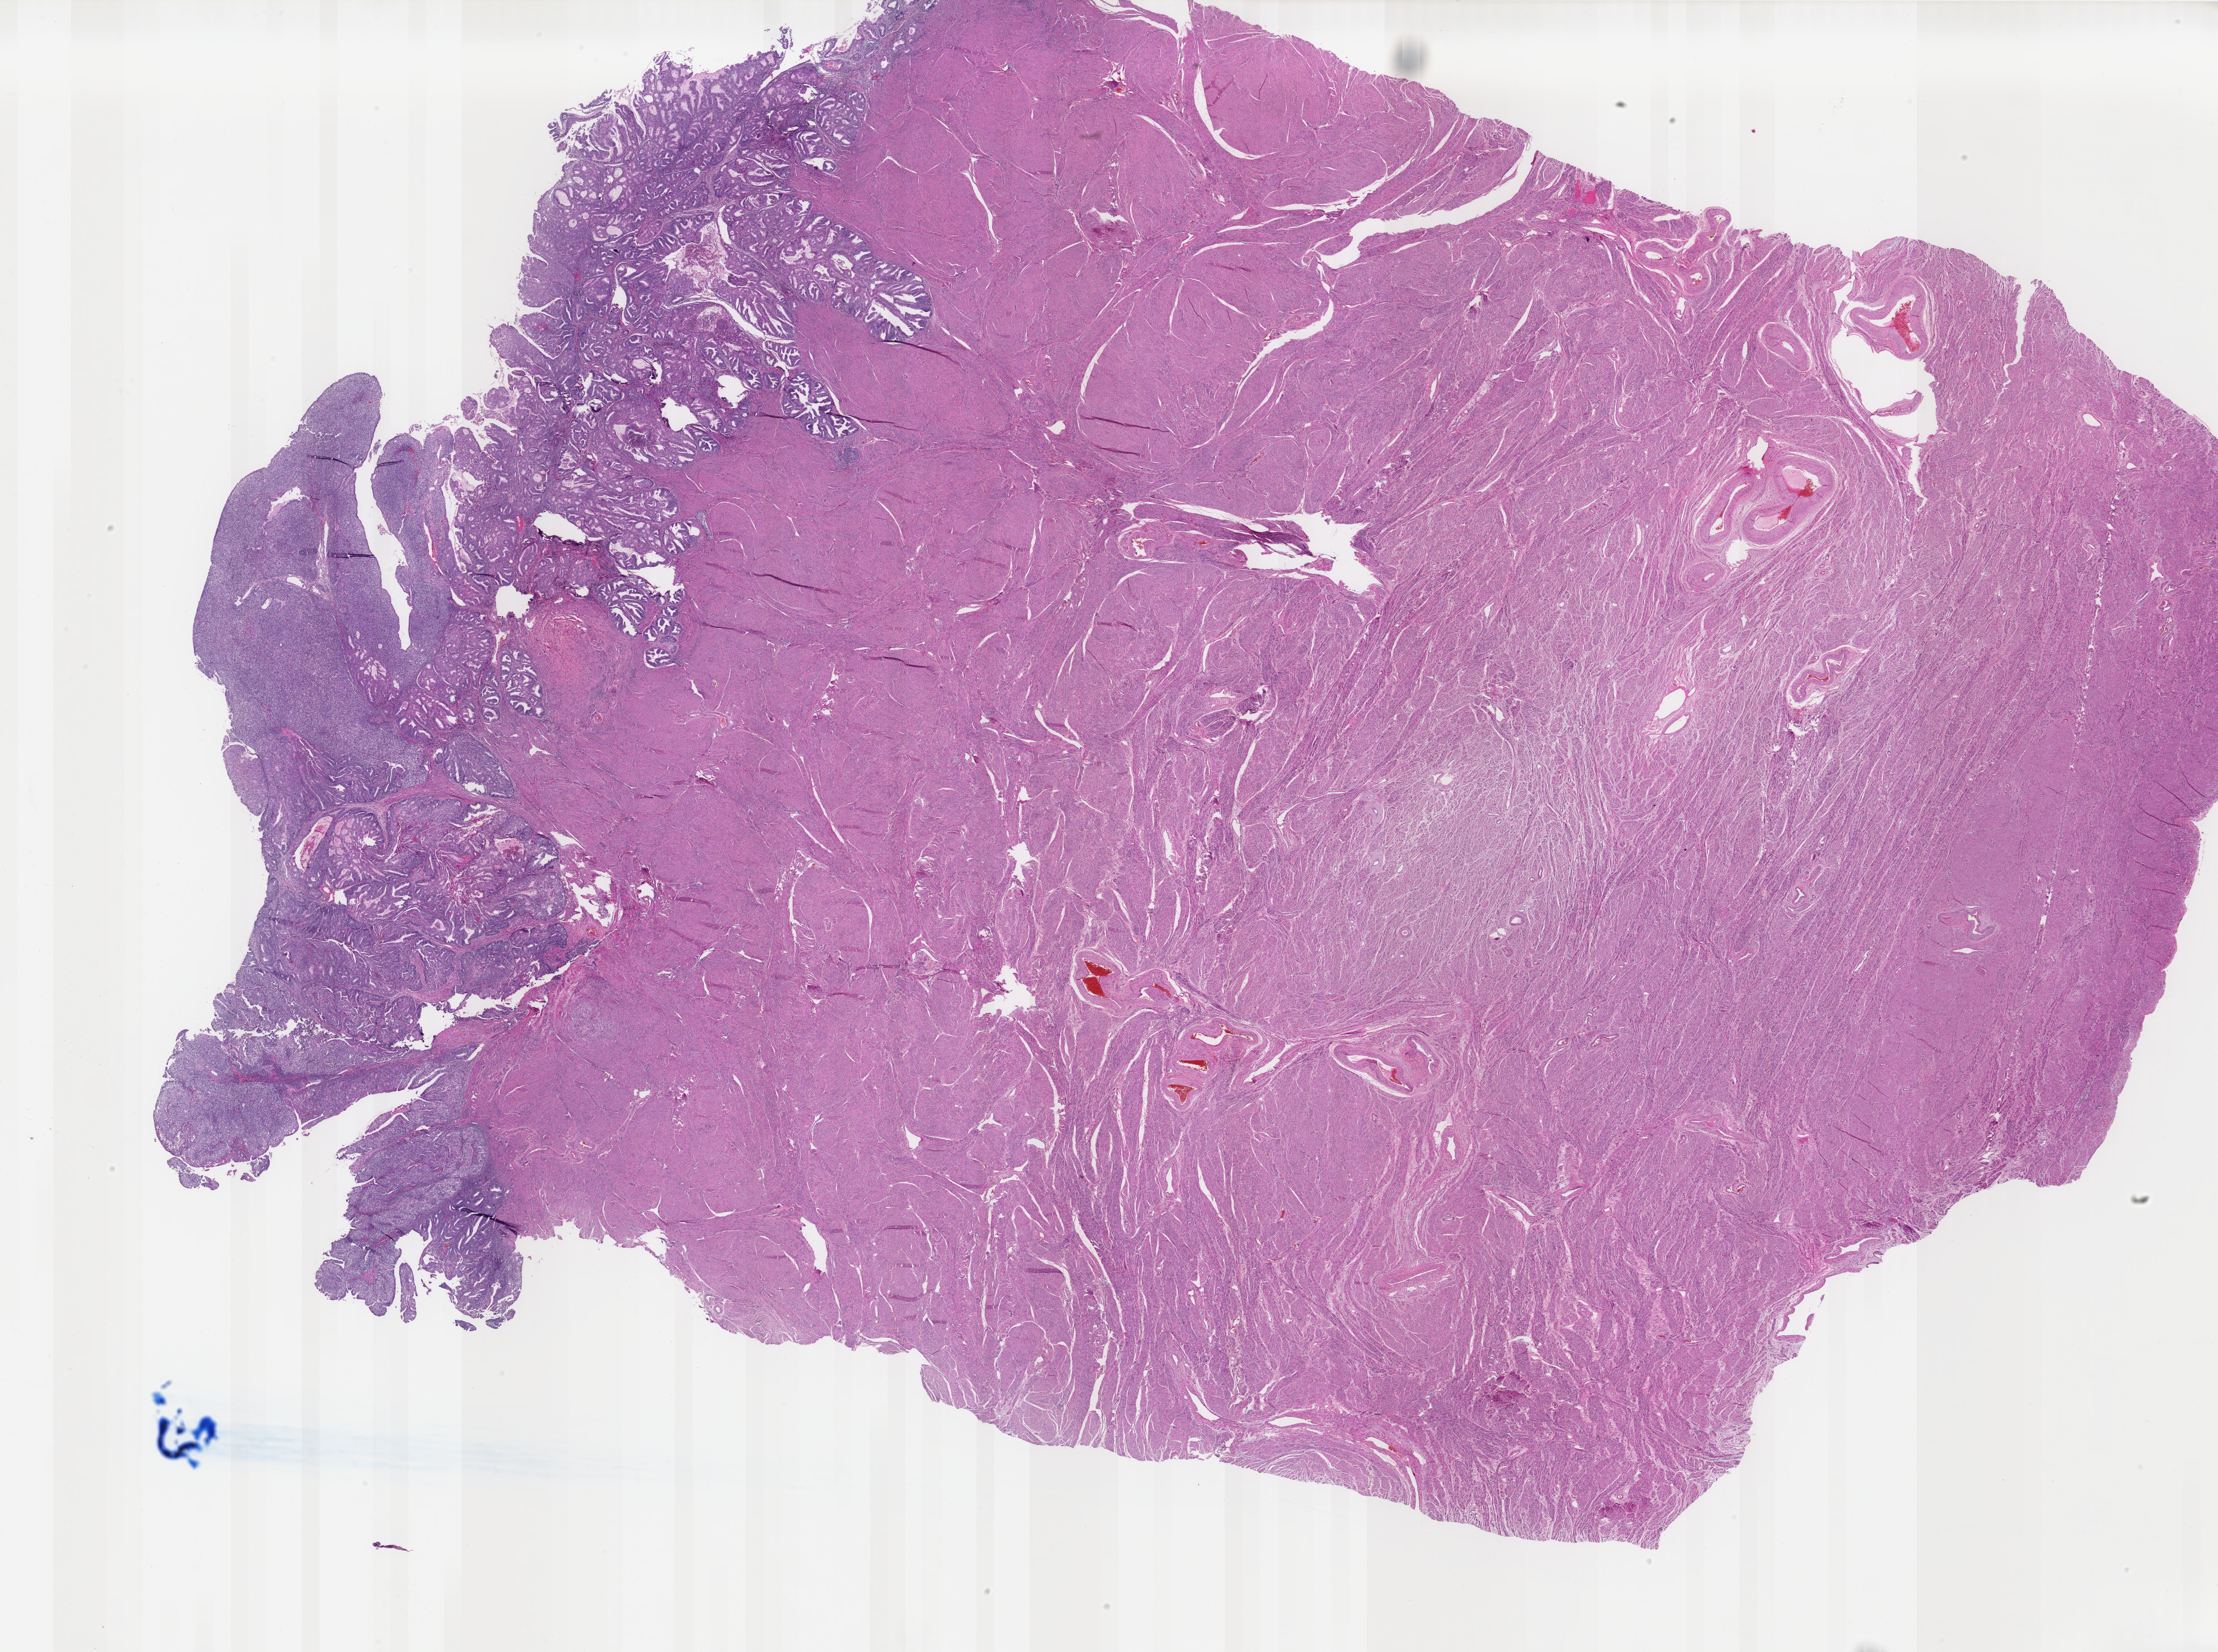
H&E-stained whole-slide image — whole scanned area (about 29.5 x 22.0 mm, from a 40x scan) shown as a low-resolution overview; FFPE section; uterus, primary tumour sample. Patient: female, age at initial diagnosis 64 years. Histologic grade: G2 (moderately differentiated).
FIGO stage: IA. Lymph nodes positive (case pathology): 0 of 17 examined. Pathologic diagnosis: Endometrioid adenocarcinoma, NOS (endometrium).